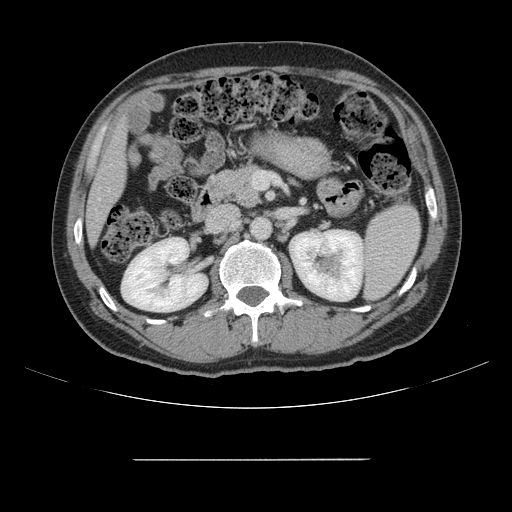
Contrast-enhanced abdominal CT, one axial slice; slice 64 of 164 in the series (ordered by position); intravenous contrast given; soft-tissue window (W 400 / L 40 HU); 2.5 mm slice thickness; 512 × 512 image matrix, field of view 404 × 404 mm. Male patient, age 54 years. From the clinical record (not read from this slice): diagnosis: colorectal cancer liver metastases, imaged before liver resection; multiple liver metastases: yes; largest metastasis: 1 cm; chemotherapy before resection: yes.
Outlined on this slice (manually delineated by an expert):
- hepatic veins: bounding box (x1, y1, x2, y2) in pixels: (99, 198, 101, 200)
- liver: (87, 127, 125, 239)
- planned liver remnant (the part of the liver to remain after resection): (87, 126, 125, 239)